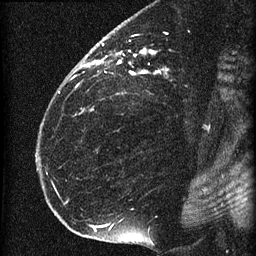
Breast MRI (dynamic contrast-enhanced), one sagittal slice; slice 43 of 60 in the series (ordered by position); dynamic contrast-enhanced series, image 2 of 4 at this slice position (ordered by acquisition); 1.5 T; TE 4.2 ms, TR 22.7 ms; 256 × 256 image matrix, field of view 180 × 180 mm. Patient: female, 35 years. Case-level facts recorded for this patient, not image findings: setting: breast cancer imaged before/during neoadjuvant chemotherapy; receptor status: HR-positive, HER2-negative.
Outlined on this slice (semi-automatically segmented with operator editing):
- analysis volume of interest (the breast-tissue region the enhancement analysis was run in; not a lesion): bounding box <69,27,198,112> (left, top, right, bottom; pixels)
- tumour enhancement mask (voxels above the 90 % enhancement threshold inside the analysis volume of interest): <73,44,168,110>